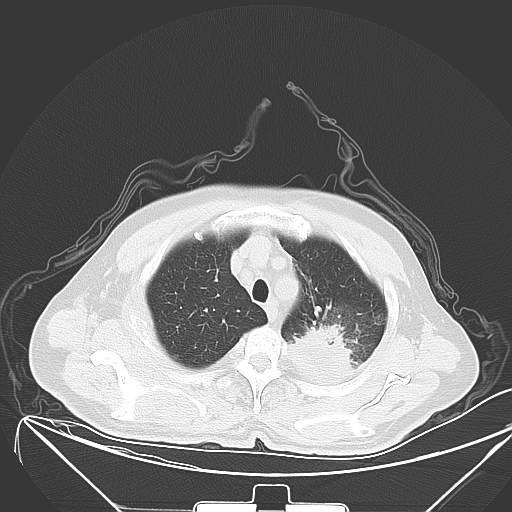
Chest CT, one axial slice; position 49 of 64 along the scan axis; lung window (W 1500 / L -600 HU); 5 mm slice thickness; 512 × 512 image matrix, field of view 431 × 431 mm. Male patient, age 58 years. Case-level facts recorded for this patient, not image findings: clinical TNM (as recorded): T2b N3 M1b.
Annotated regions visible in this slice (rectangle marked by the reading radiologist):
- lung tumour (recorded histology: adenocarcinoma): box from (x=286, y=317) to (x=354, y=388) px